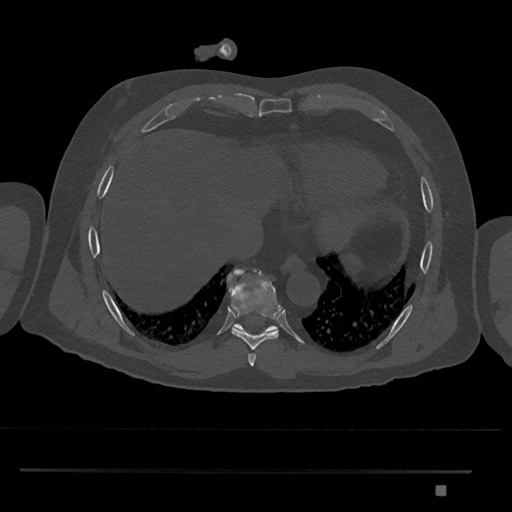
CT including the spine, one axial slice; position 1095 of 1134 along the scan axis; reconstruction kernel Br40s/3; 120 kVp; bone window (W 1800 / L 400 HU); 0.5 mm slice thickness; 512 × 512 image matrix, field of view 429 × 429 mm. Male patient, age 65 years. From the clinical record (not read from this slice): primary cancer: prostate.
Outlined on this slice (semi-automatically segmented with operator editing):
- T8 vertebra: box from (x=229, y=269) to (x=283, y=349) px
- T9 vertebra: (x=227, y=271)–(x=278, y=333)